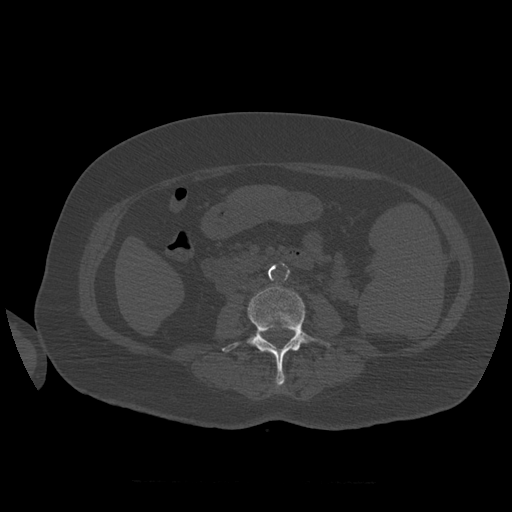
CT including the spine, one axial slice; position 229 of 399 along the scan axis; reconstruction kernel STANDARD; 120 kVp; bone window (W 1800 / L 400 HU); 1.25 mm slice thickness; 512 × 512 image matrix, field of view 404 × 404 mm. Patient age 81 years. From the clinical record (not read from this slice): primary cancer: renal; vertebrae with lytic lesions (as recorded): L1.
Annotated regions visible in this slice (semi-automatic segmentation, software-assisted and operator-edited):
- L3 vertebra: box from (x=222, y=286) to (x=330, y=387) px